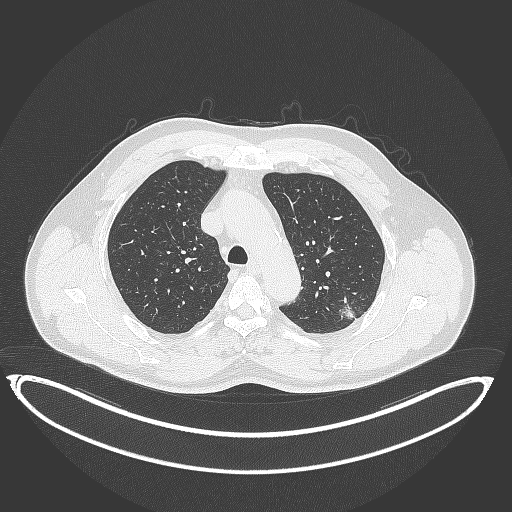
Chest CT, one axial slice. Slice 270 of 399 in the series (ordered by position). Reconstruction kernel B70f. 120 kVp. Lung window (W 1500 / L -600 HU). 1 mm slice thickness. 512 × 512 image matrix, field of view 469 × 469 mm. Patient: male, 58 years. Case-level facts recorded for this patient, not image findings: clinical TNM (as recorded): T1c N0 M0.
Structures marked on this image (rectangle marked by the reading radiologist):
- lung tumour (recorded histology: adenocarcinoma): bounding box <335,296,361,323> (left, top, right, bottom; pixels)